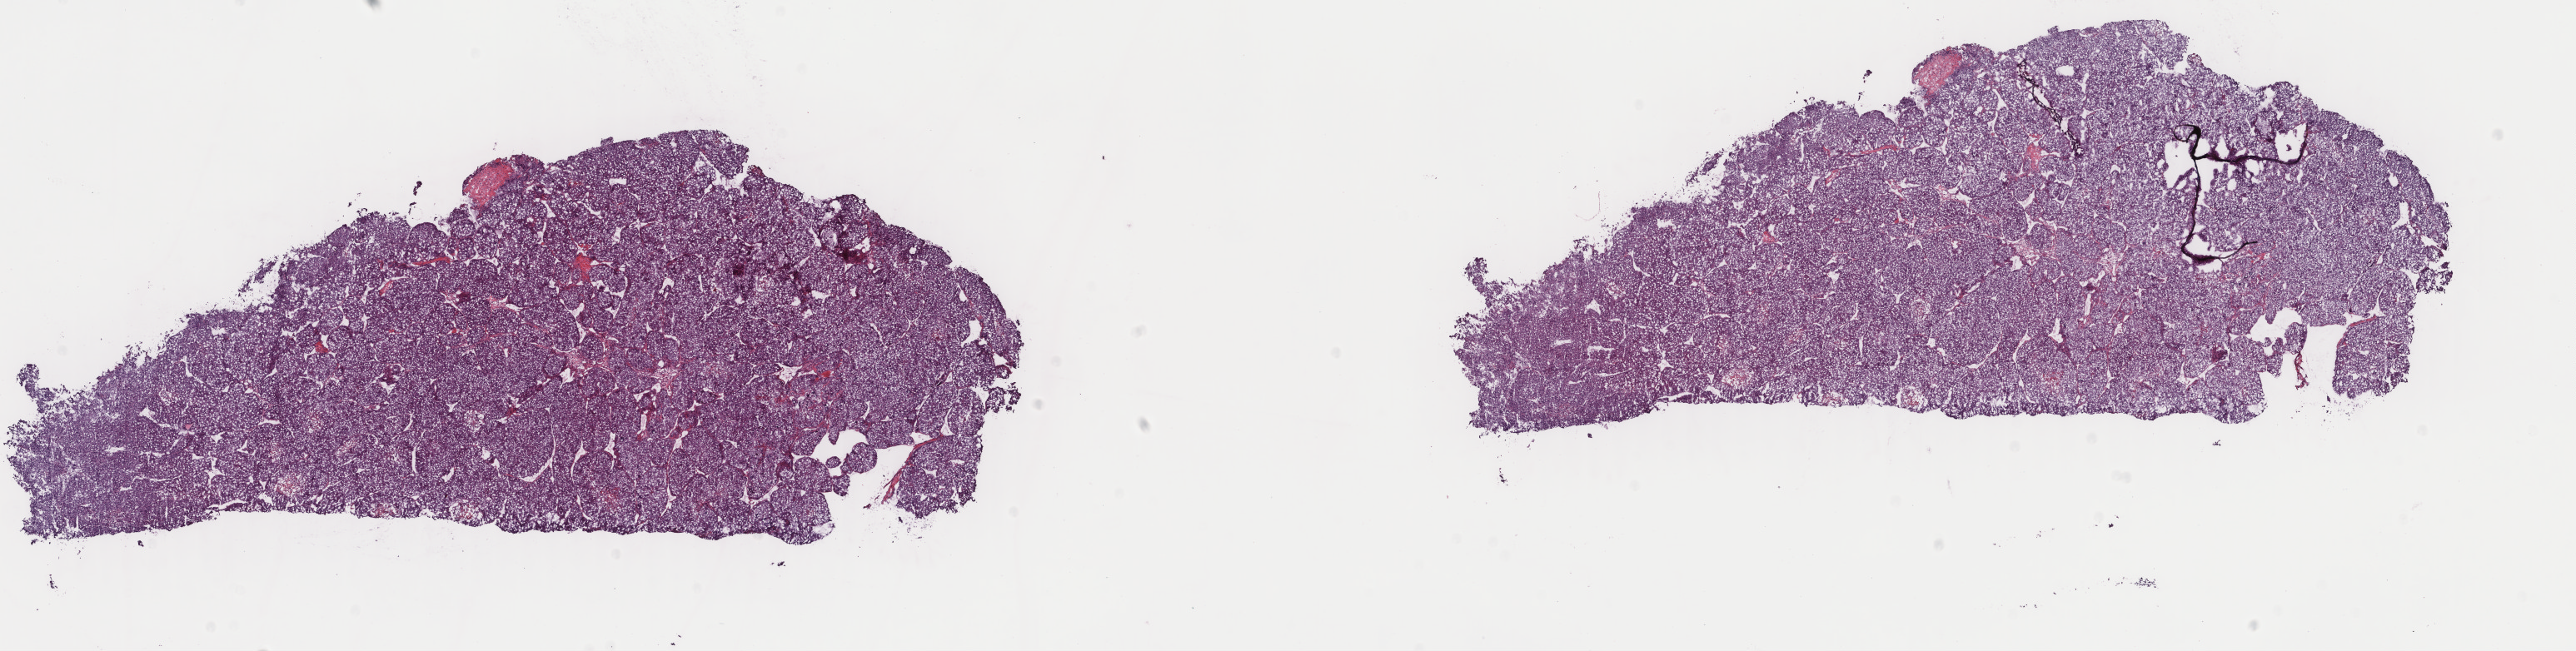
H&E-stained whole-slide image — whole scanned area (about 24.6 x 6.2 mm) shown as a low-resolution overview. Frozen section from the top of the tissue portion. Liver, primary tumour sample. Male, age 47 years at initial diagnosis. Histologic grade: G2 (moderately differentiated). Pathologist review of this section (percent, as recorded): tumour cells 100%, tumour nuclei 80%, normal cells 0%, stromal cells 0%, necrosis 0%. Inflammatory infiltration, as recorded: lymphocyte infiltration 2%, monocyte infiltration 0%, neutrophil infiltration 0%.
Diagnosis: Hepatocellular carcinoma, NOS. TNM: T2 N0 M0. AJCC pathologic stage: II (7th edition).